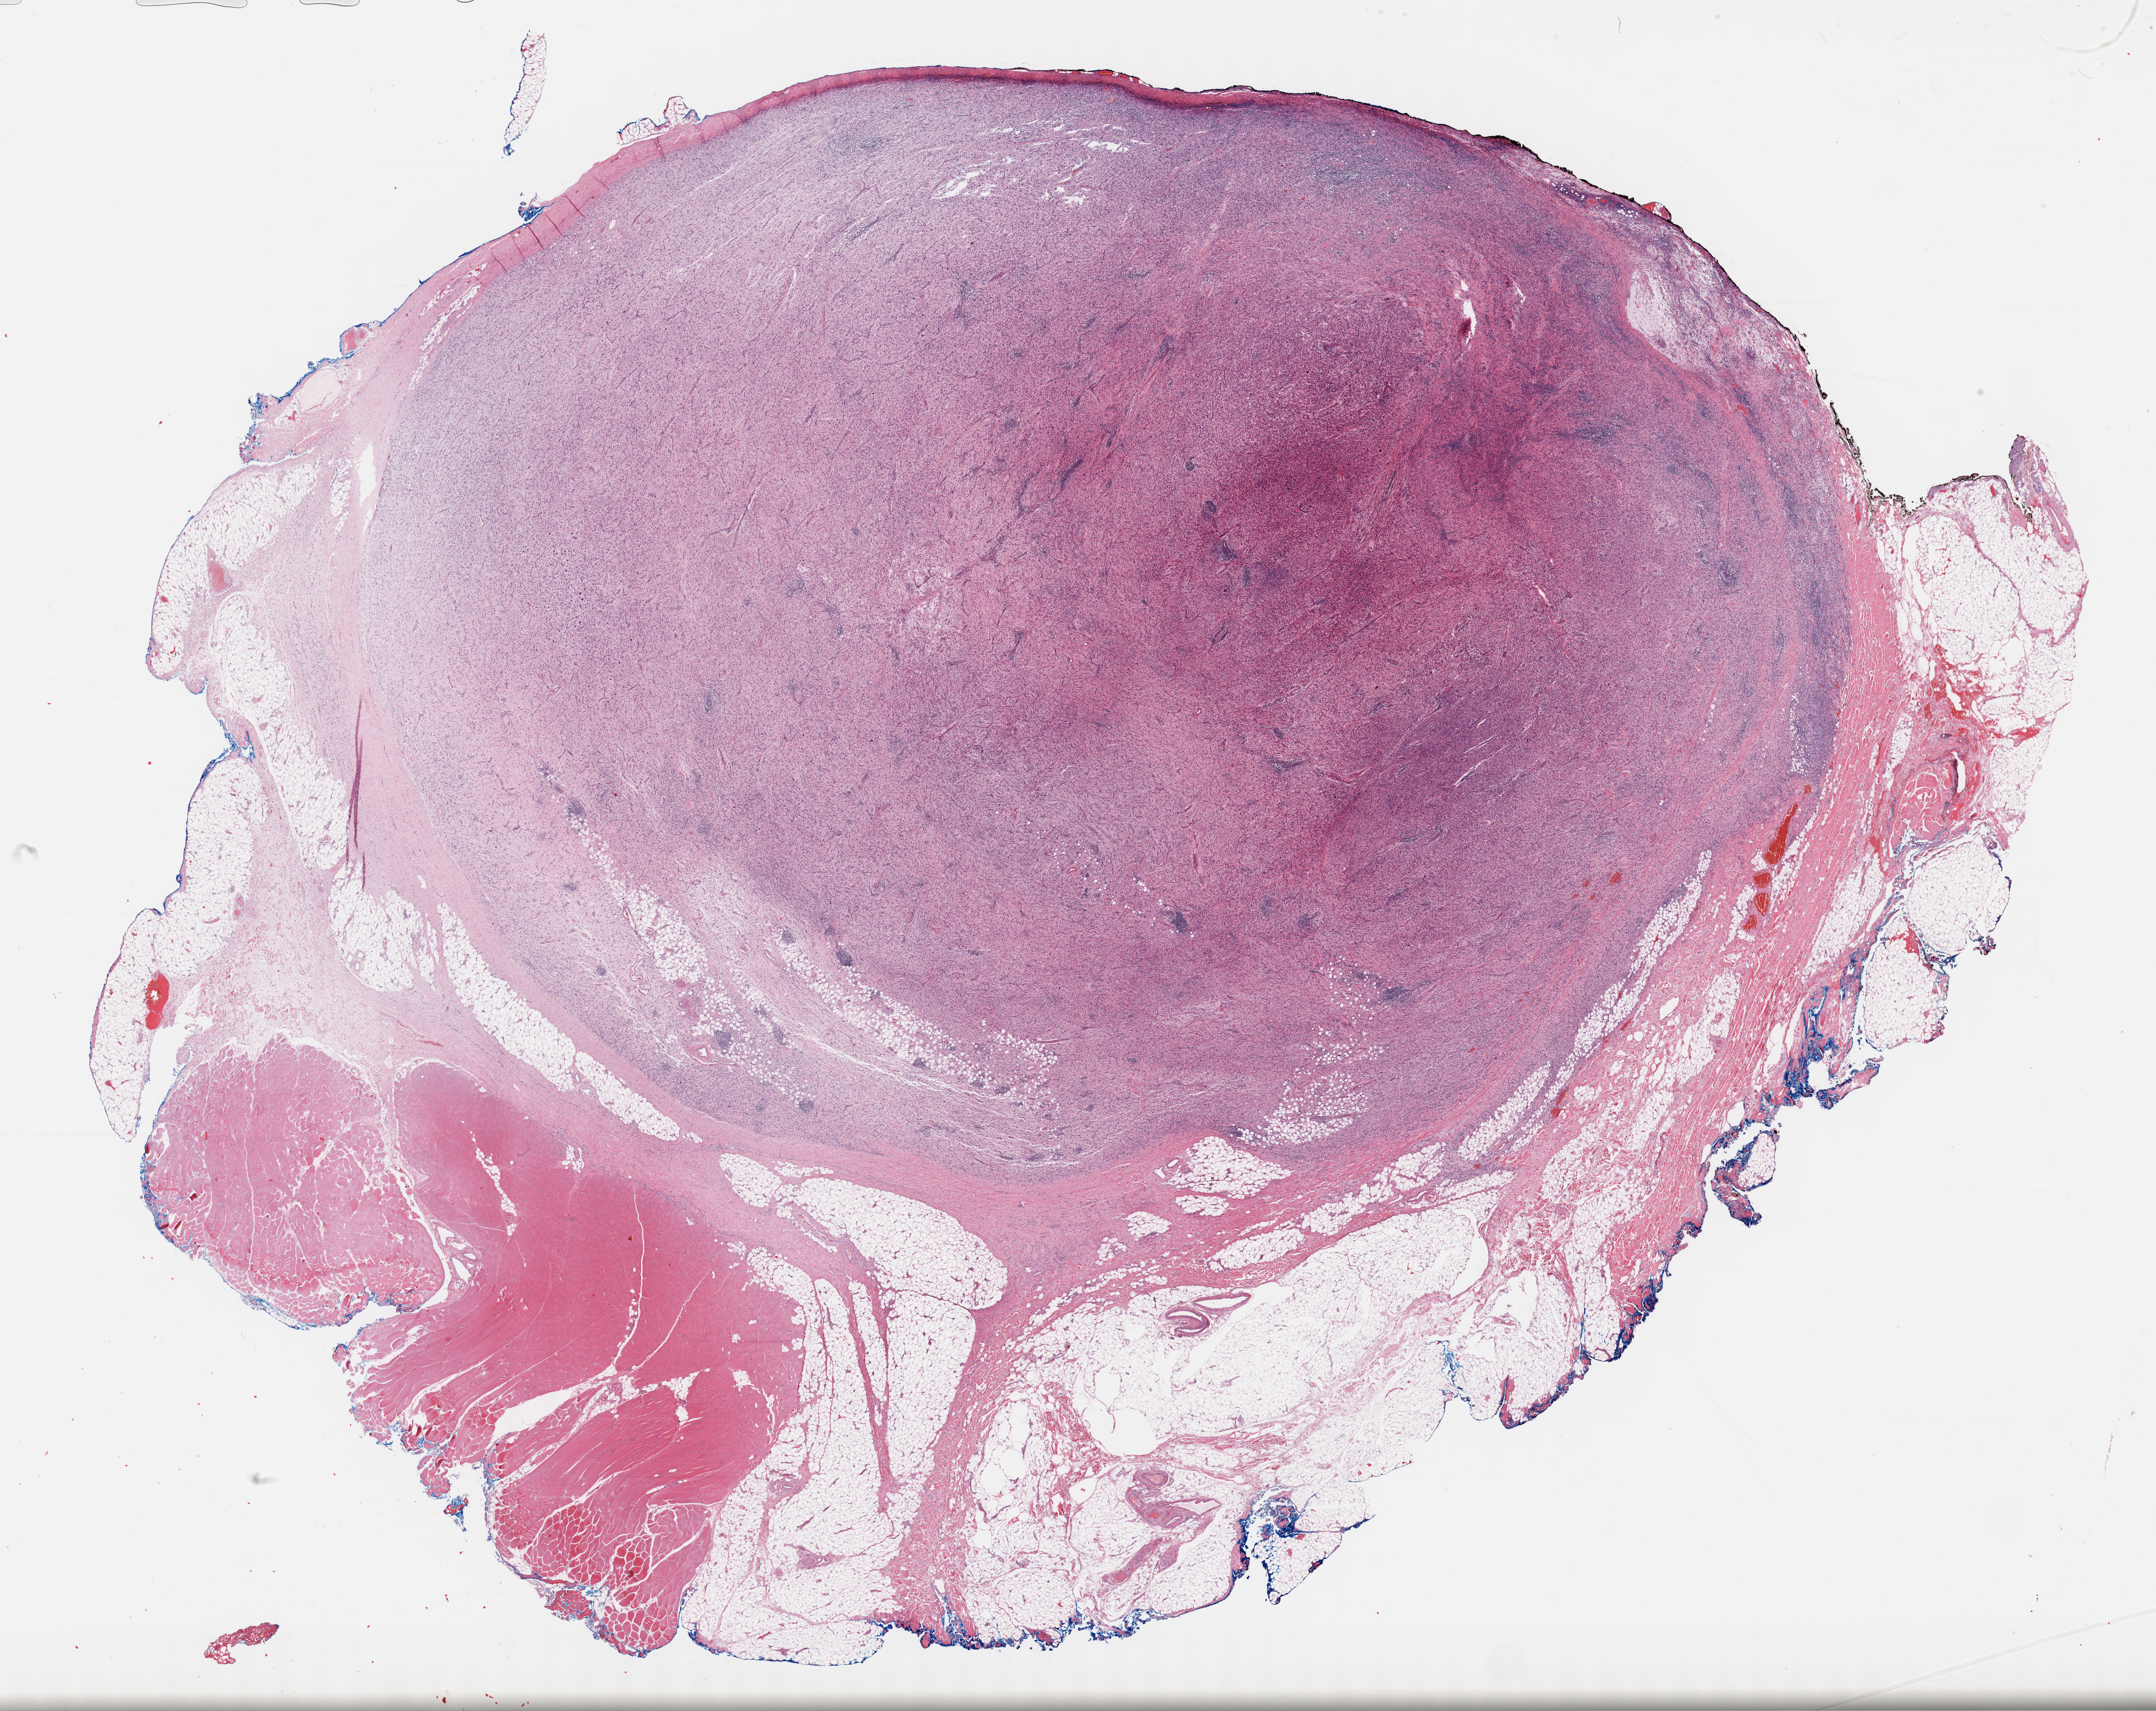
H&E whole-slide image, shown as a low-resolution overview of the whole scanned area (about 28.7 x 22.8 mm, from a 40x scan); formalin-fixed paraffin-embedded (FFPE) diagnostic section; primary tumour sample from the connective, subcutaneous and other soft tissues. Male patient; age at initial diagnosis 35 years.
Histologic diagnosis: Fibromyxosarcoma (connective, subcutaneous and other soft tissues of lower limb and hip).